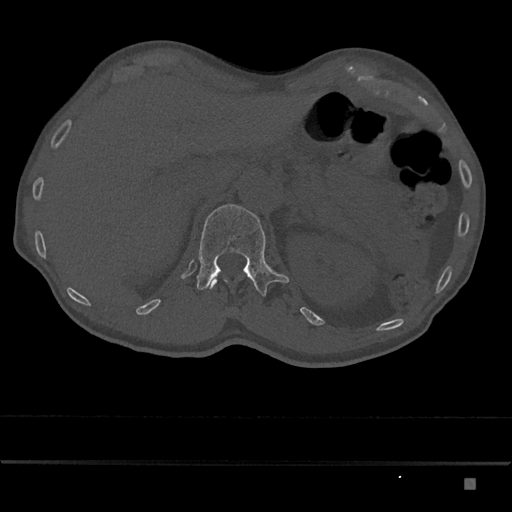
CT including the spine, one axial slice; position 562 of 797 along the scan axis; reconstruction kernel Br40s/3; 120 kVp; bone window (W 1800 / L 400 HU); 0.5 mm slice thickness; 512 × 512 image matrix, field of view 390 × 390 mm. Patient: male, 72 years. Case-level facts recorded for this patient, not image findings: primary cancer: prostate.
Annotated regions visible in this slice (semi-automatically segmented with operator editing):
- L1 vertebra: bounding box <197,204,289,297> (left, top, right, bottom; pixels)
- T12 vertebra: <208,277,228,289>